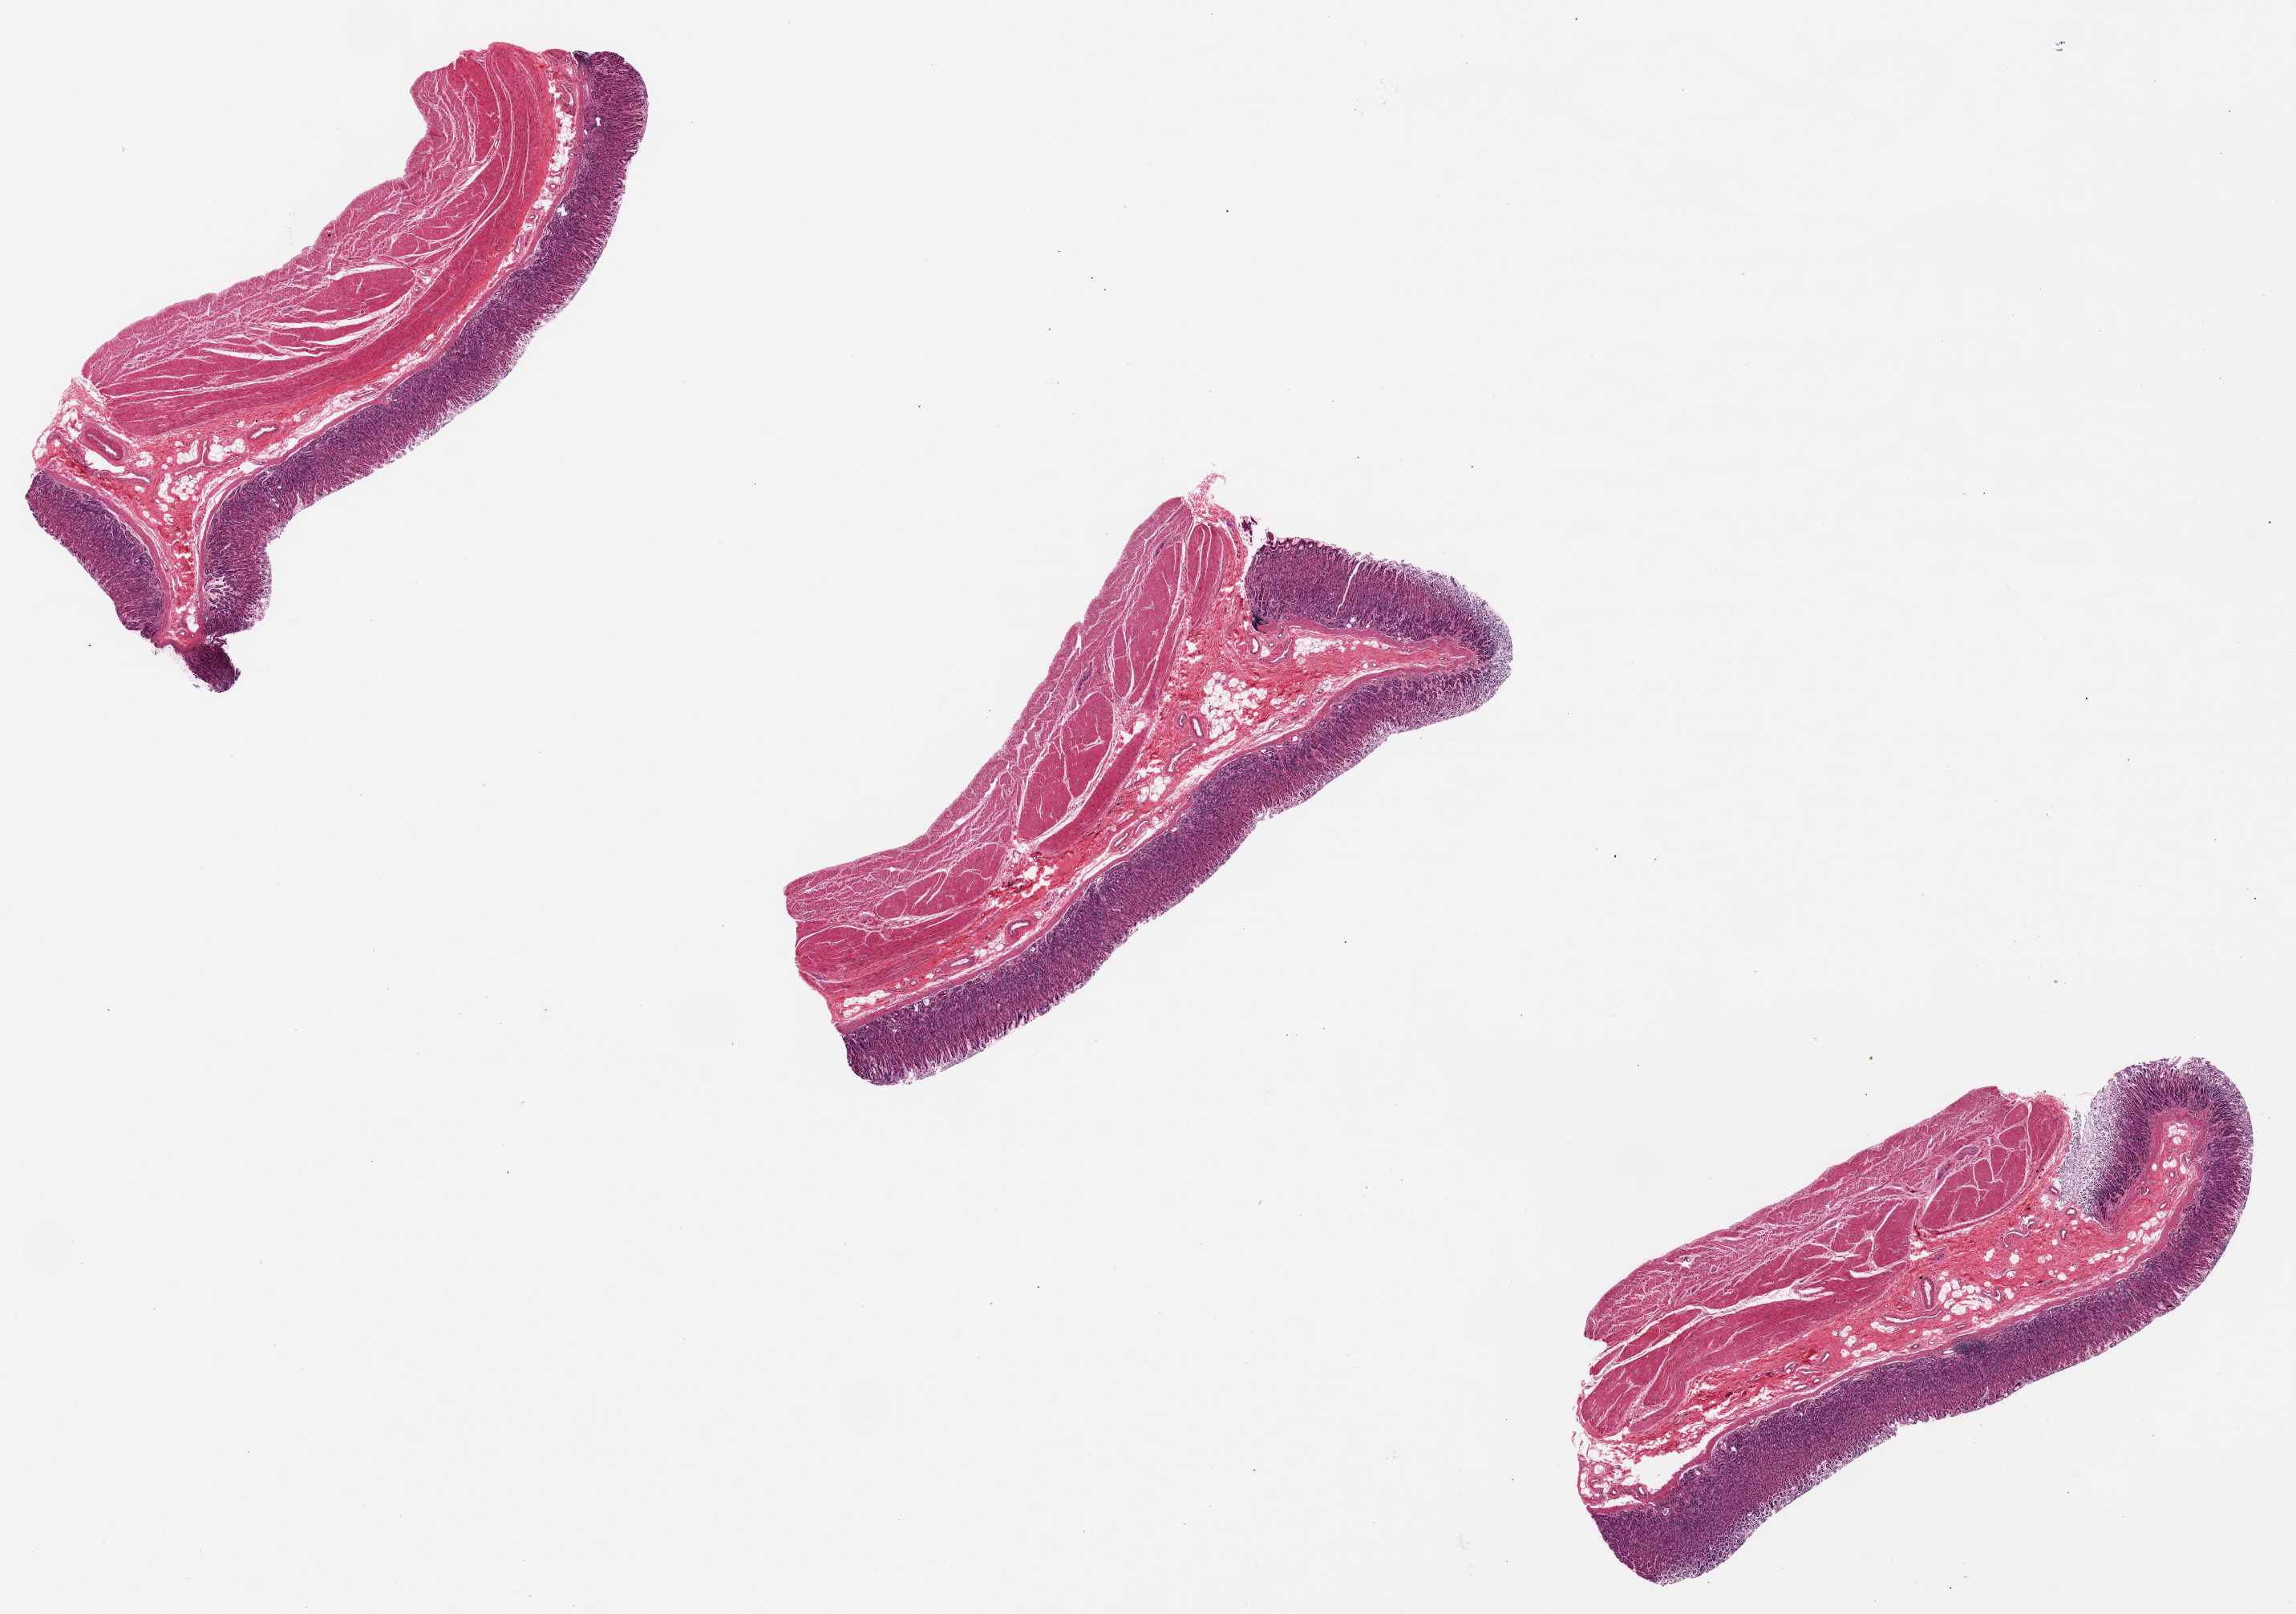
Whole-slide image, haematoxylin and eosin stain, whole scanned area (about 22.6 x 15.9 mm) shown as a low-resolution overview, PAXgene-fixed paraffin-embedded (PFPE) section, section of stomach (target tissue), tissue donor sample. Donor: female.
Review note (as recorded): deep mucosa well preserved; surface autolyzed. 7x3mm.